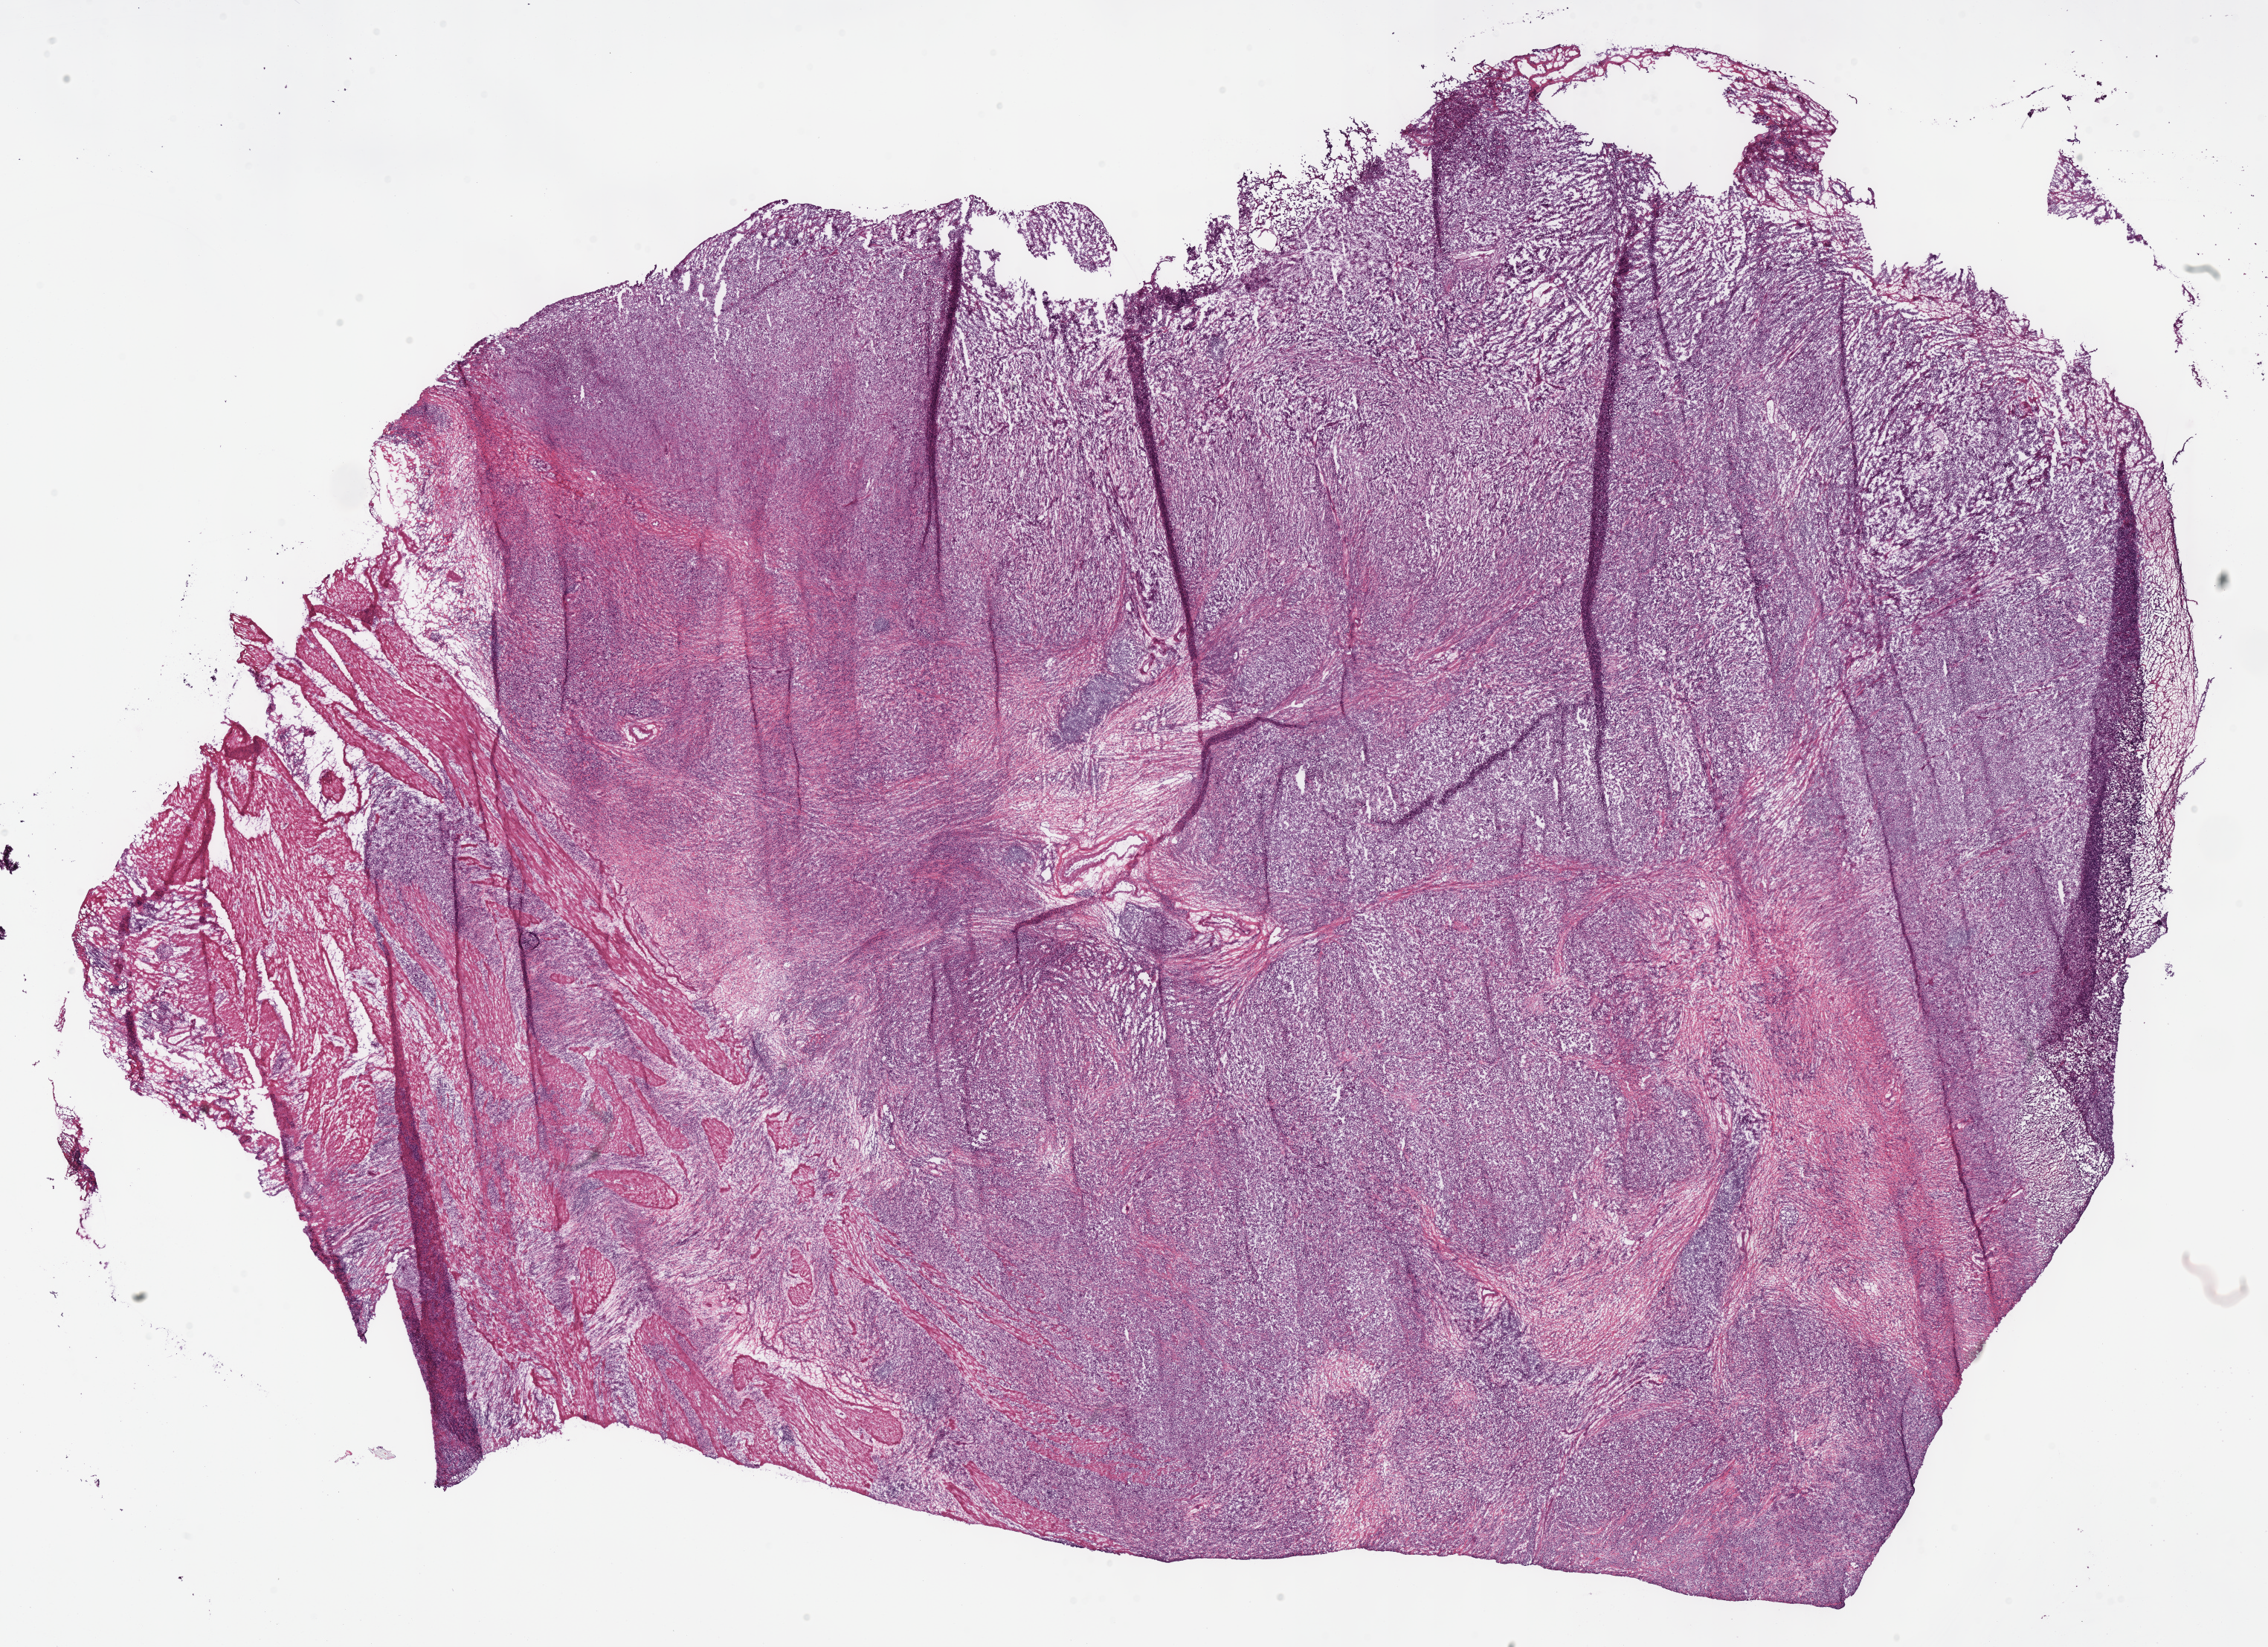
Hematoxylin and eosin (H&E) stained whole-slide image, low-resolution overview of the scanned area, about 24.0 x 17.4 mm, frozen section, sample: primary tumour, stomach. Female, age 72 years at initial diagnosis. Histologic grade: G3 (poorly differentiated). Pathologist review of this section (percent, as recorded): tumour cells 80%, tumour nuclei 75%, normal cells 0%, stromal cells 20%, necrosis 0%.
Lymph nodes positive (case pathology): 9 of 9 examined. TNM: T4a N3a M0. Pathologic diagnosis: Adenocarcinoma, intestinal type (gastric antrum). AJCC pathologic stage: IIIC (7th edition).